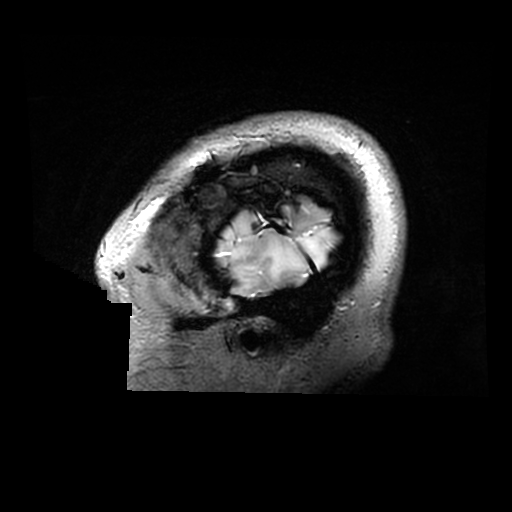
Brain MRI from a brain-tumour surgery series, one sagittal slice. Position 257 of 320 along the scan axis. 0.6 mm slice thickness. 512 × 512 image matrix. From the clinical record (not read from this slice): histopathology: Astrocytoma; WHO grade: 2; IDH mutation: yes.
Outlined on this slice (manually delineated by an expert):
- tumour: bounding box (x1, y1, x2, y2) in pixels: (217, 214, 338, 283)